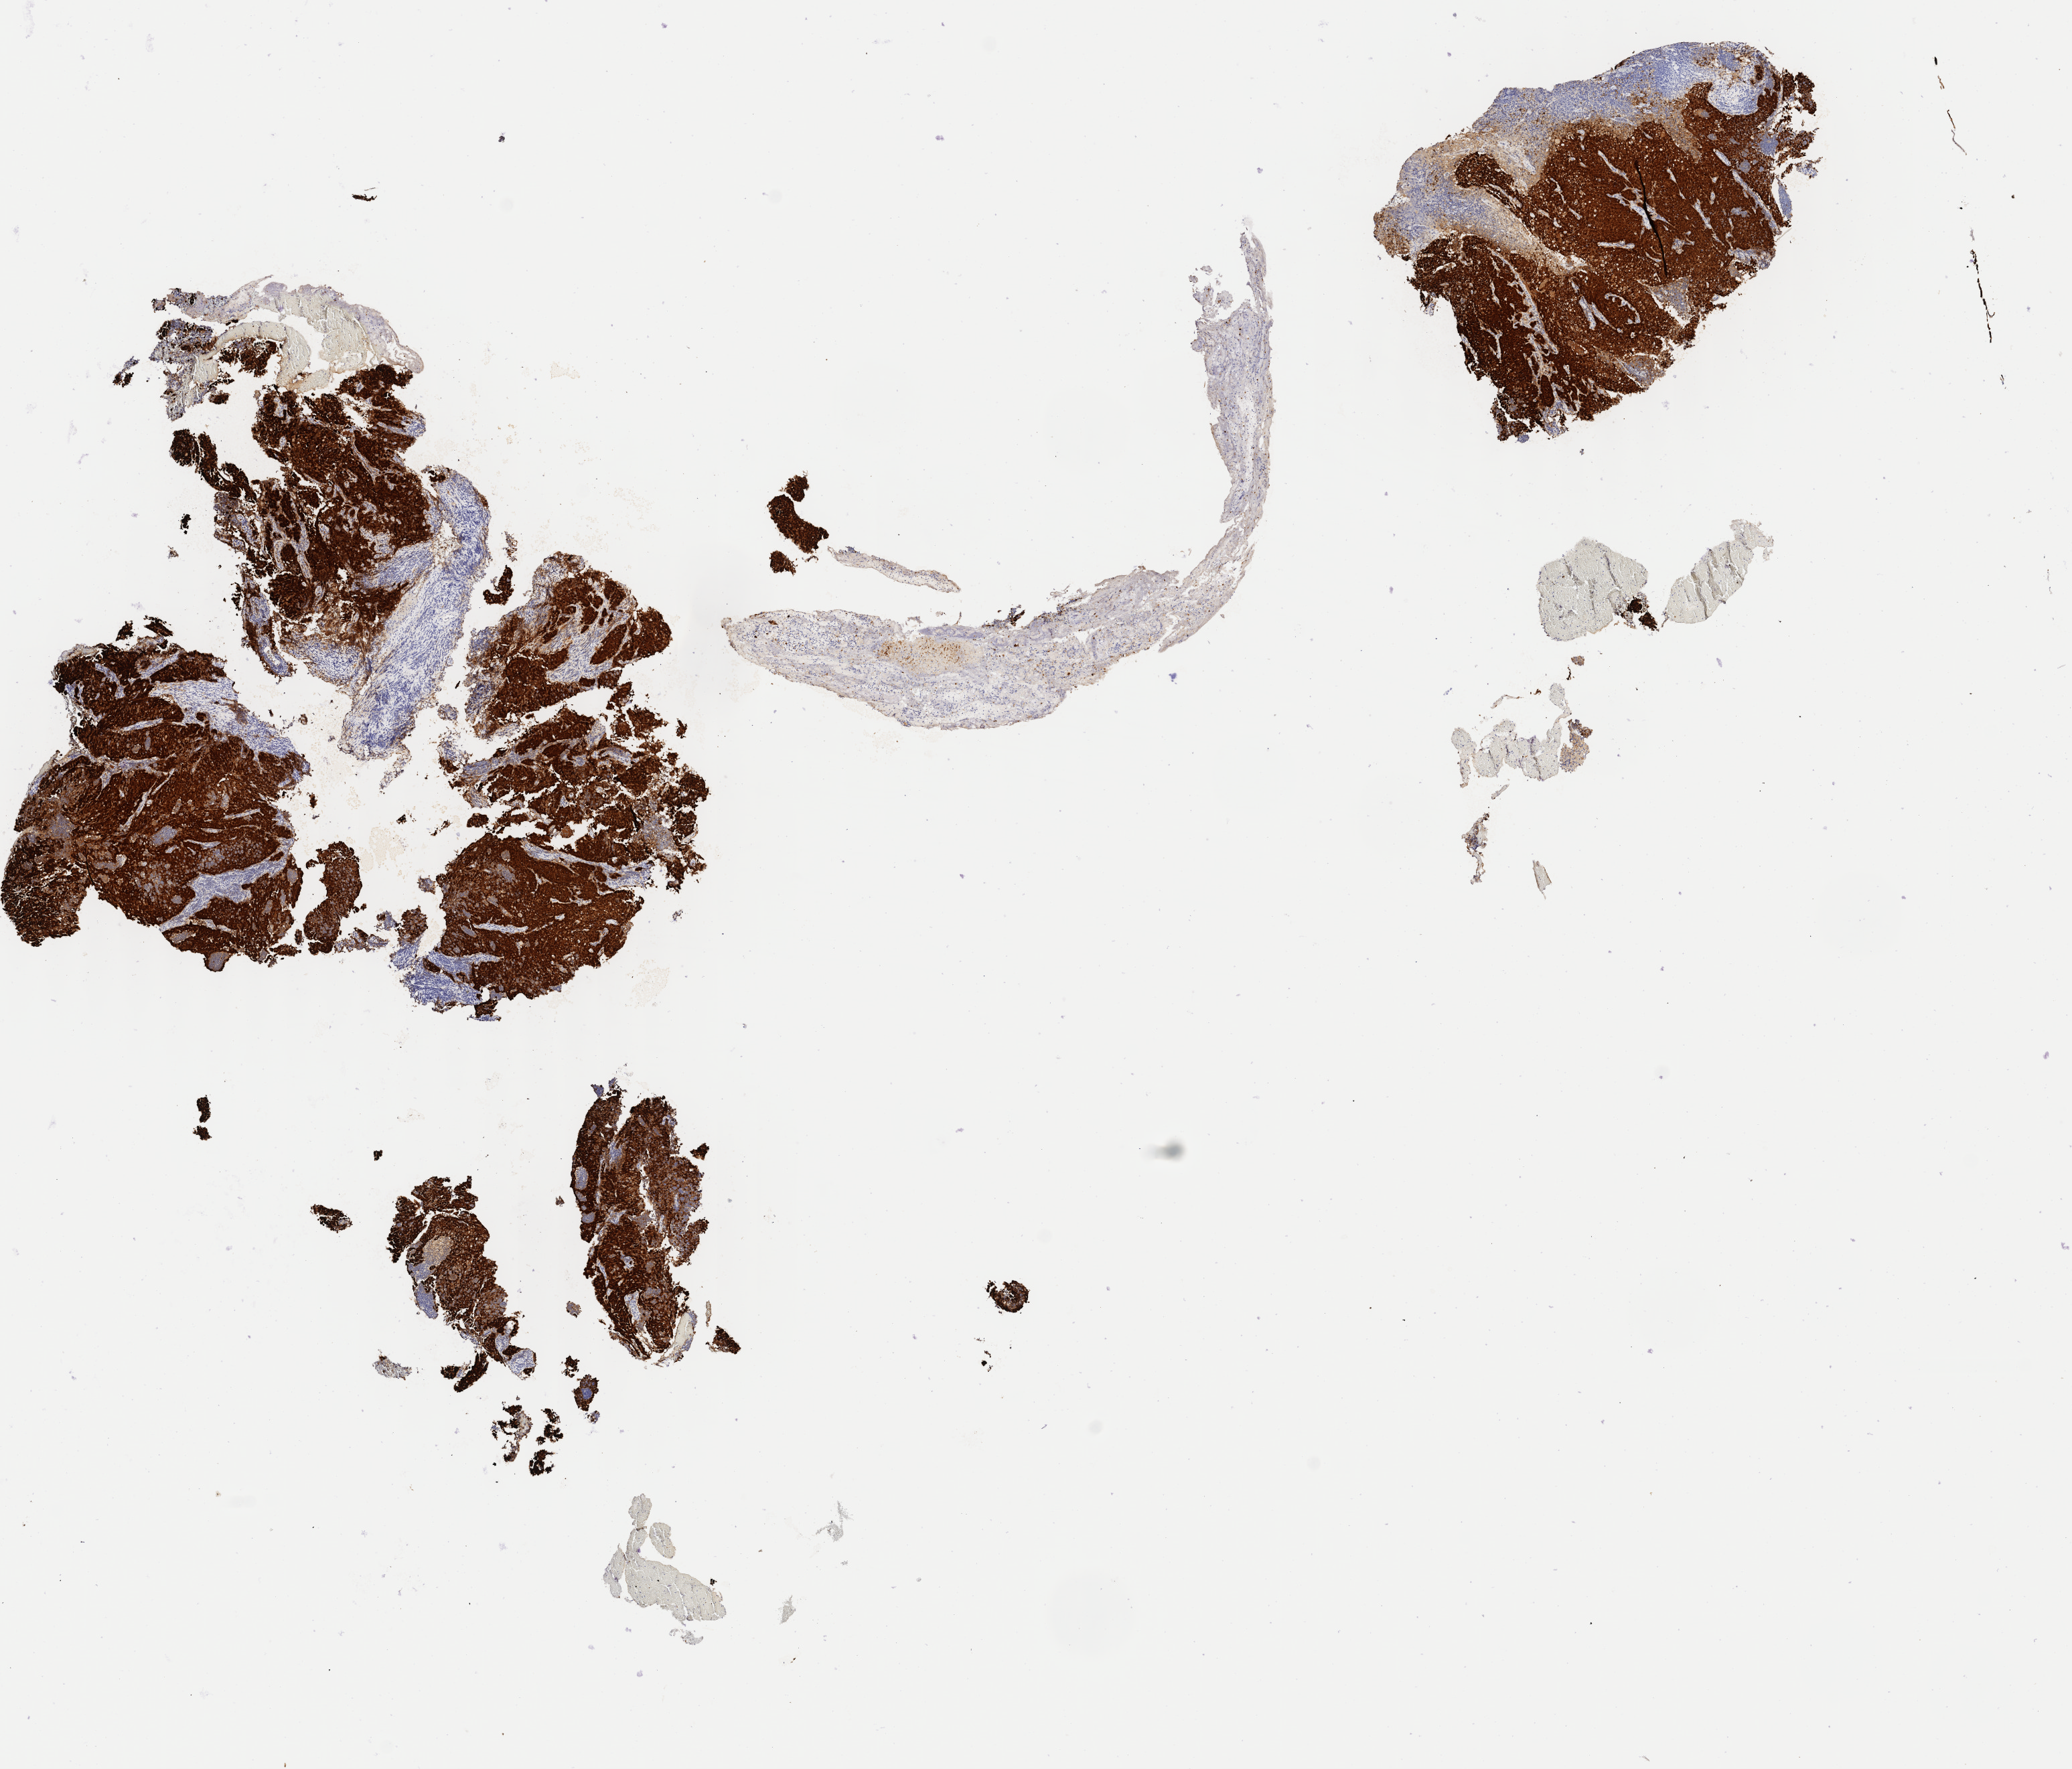
Whole-slide image, immunohistochemical stain for p16 (p16INK4a), low-resolution overview of the scanned area, about 12.3 x 10.5 mm; specimen: tumor tissue; anatomic site: cervix. Female patient, 33 years old.
Diagnosis: Squamous cell carcinoma, large cell, nonkeratinizing, NOS.